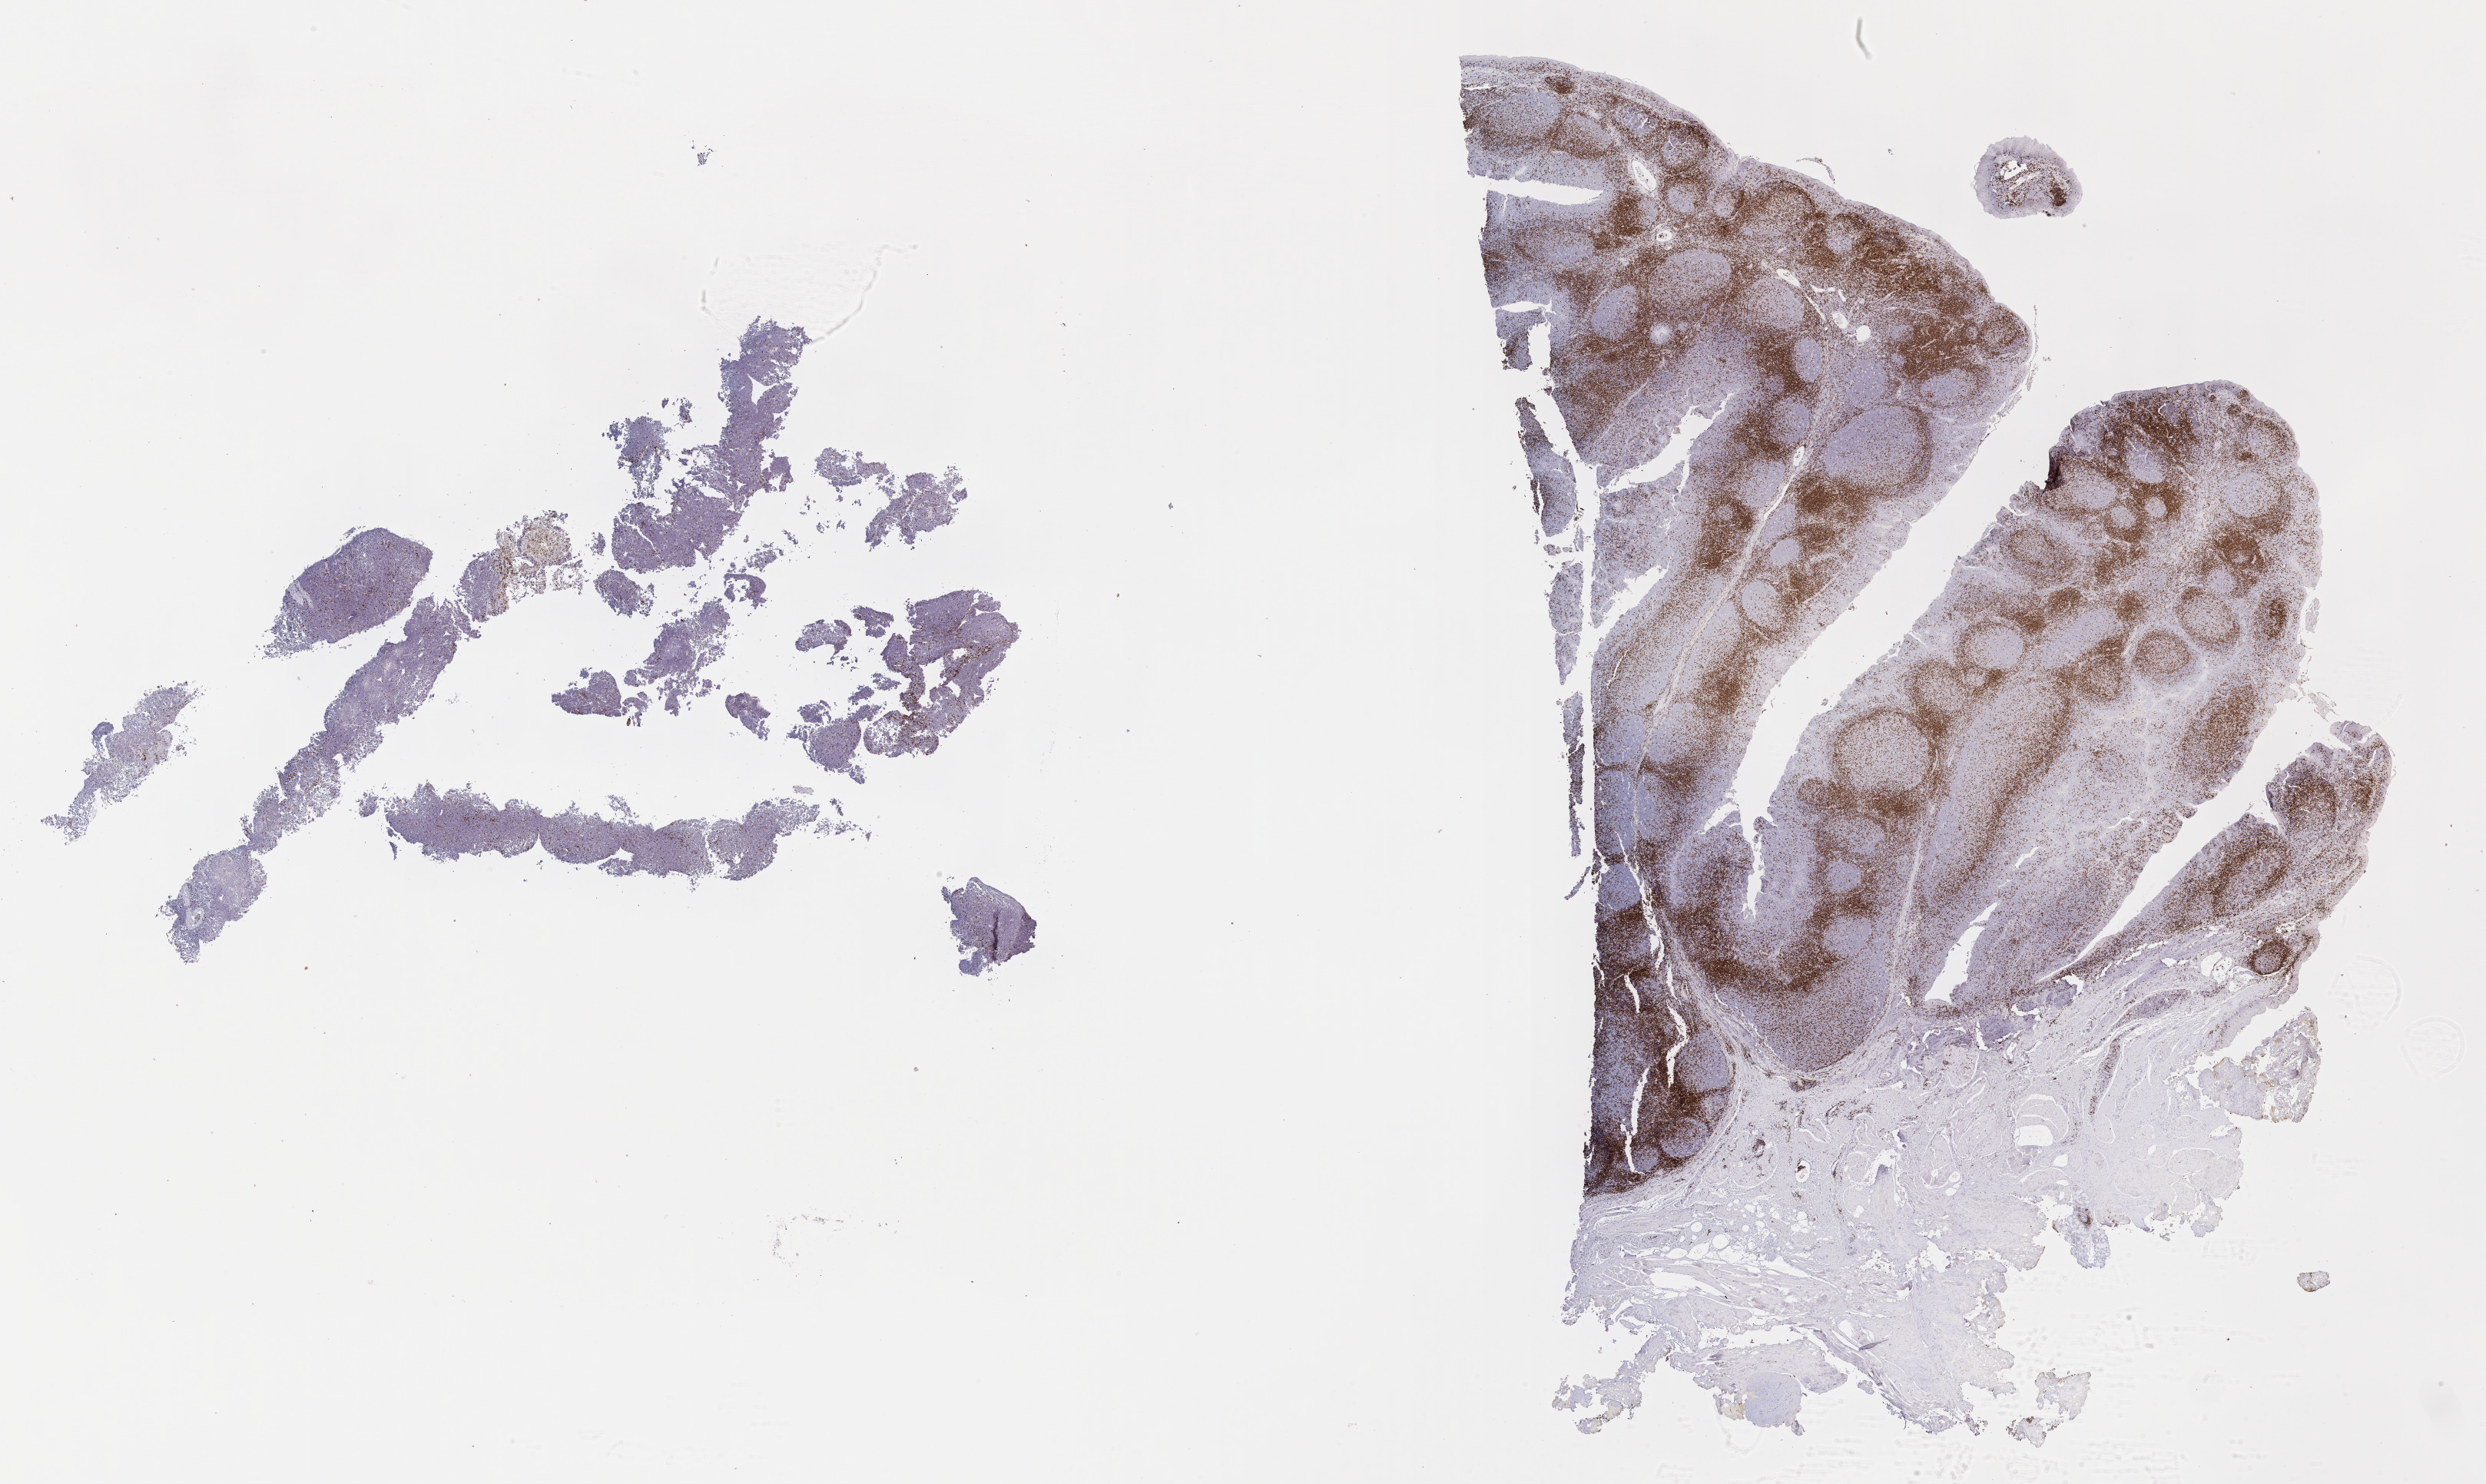
Whole-slide image, immunohistochemical stain for CD3 — whole scanned area (about 26.2 x 15.6 mm) shown as a low-resolution overview. Tumor tissue. Anatomic site: kidney. Male patient; age at initial diagnosis 3 years.
Histologic diagnosis: Burkitt lymphoma, NOS.